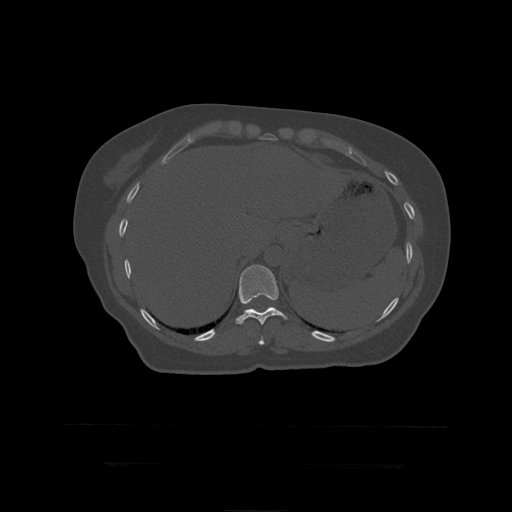
CT including the spine, one axial slice; slice 220 of 399 in the series (ordered by position); reconstruction kernel STANDARD; bone window (W 1800 / L 400 HU); 1.25 mm slice thickness; 512 × 512 image matrix. Patient age 41 years. Case-level facts recorded for this patient, not image findings: primary cancer: breast.
Outlined on this slice (semi-automatic segmentation, software-assisted and operator-edited):
- T10 vertebra: bounding box <259,336,265,345> (left, top, right, bottom; pixels)
- T11 vertebra: <236,265,288,325>